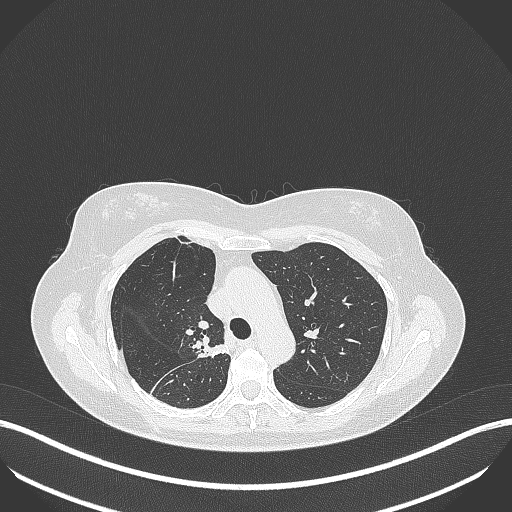
Chest CT, one axial slice. Slice 275 of 386 in the series (ordered by position). Lung window (W 1500 / L -600 HU). 1 mm slice thickness. 512 × 512 image matrix, field of view 400 × 400 mm. Female patient, age 65 years. Case-level facts recorded for this patient, not image findings: clinical TNM (as recorded): T1b N0 M0; histopathological grade: G2.
Annotated regions visible in this slice (bounding box drawn by a radiologist):
- lung tumour (recorded histology: adenocarcinoma): bounding box (x1, y1, x2, y2) in pixels: (190, 339, 230, 360)